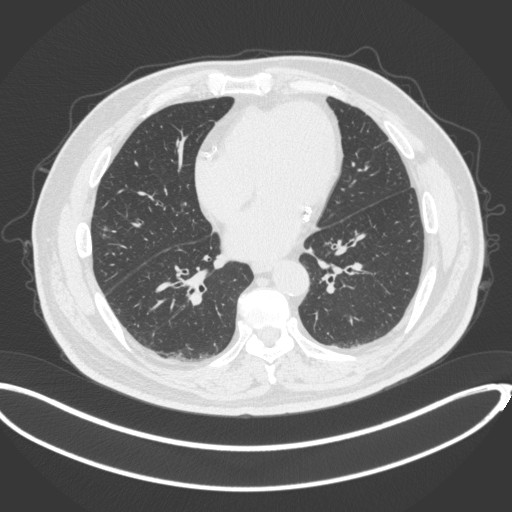
Chest CT, one axial slice; slice 133 of 342 in the series (ordered by position); 120 kVp; lung window (W 1500 / L -600 HU); 1 mm slice thickness; 512 × 512 image matrix, field of view 427 × 427 mm. Patient: male, 68 years. Case-level facts recorded for this patient, not image findings: clinical TNM (as recorded): T1c N0 M0; histopathological grade: G2.
Structures marked on this image (bounding box drawn by a radiologist):
- lung tumour (recorded histology: adenocarcinoma): bounding box (x1, y1, x2, y2) in pixels: (102, 224, 116, 239)